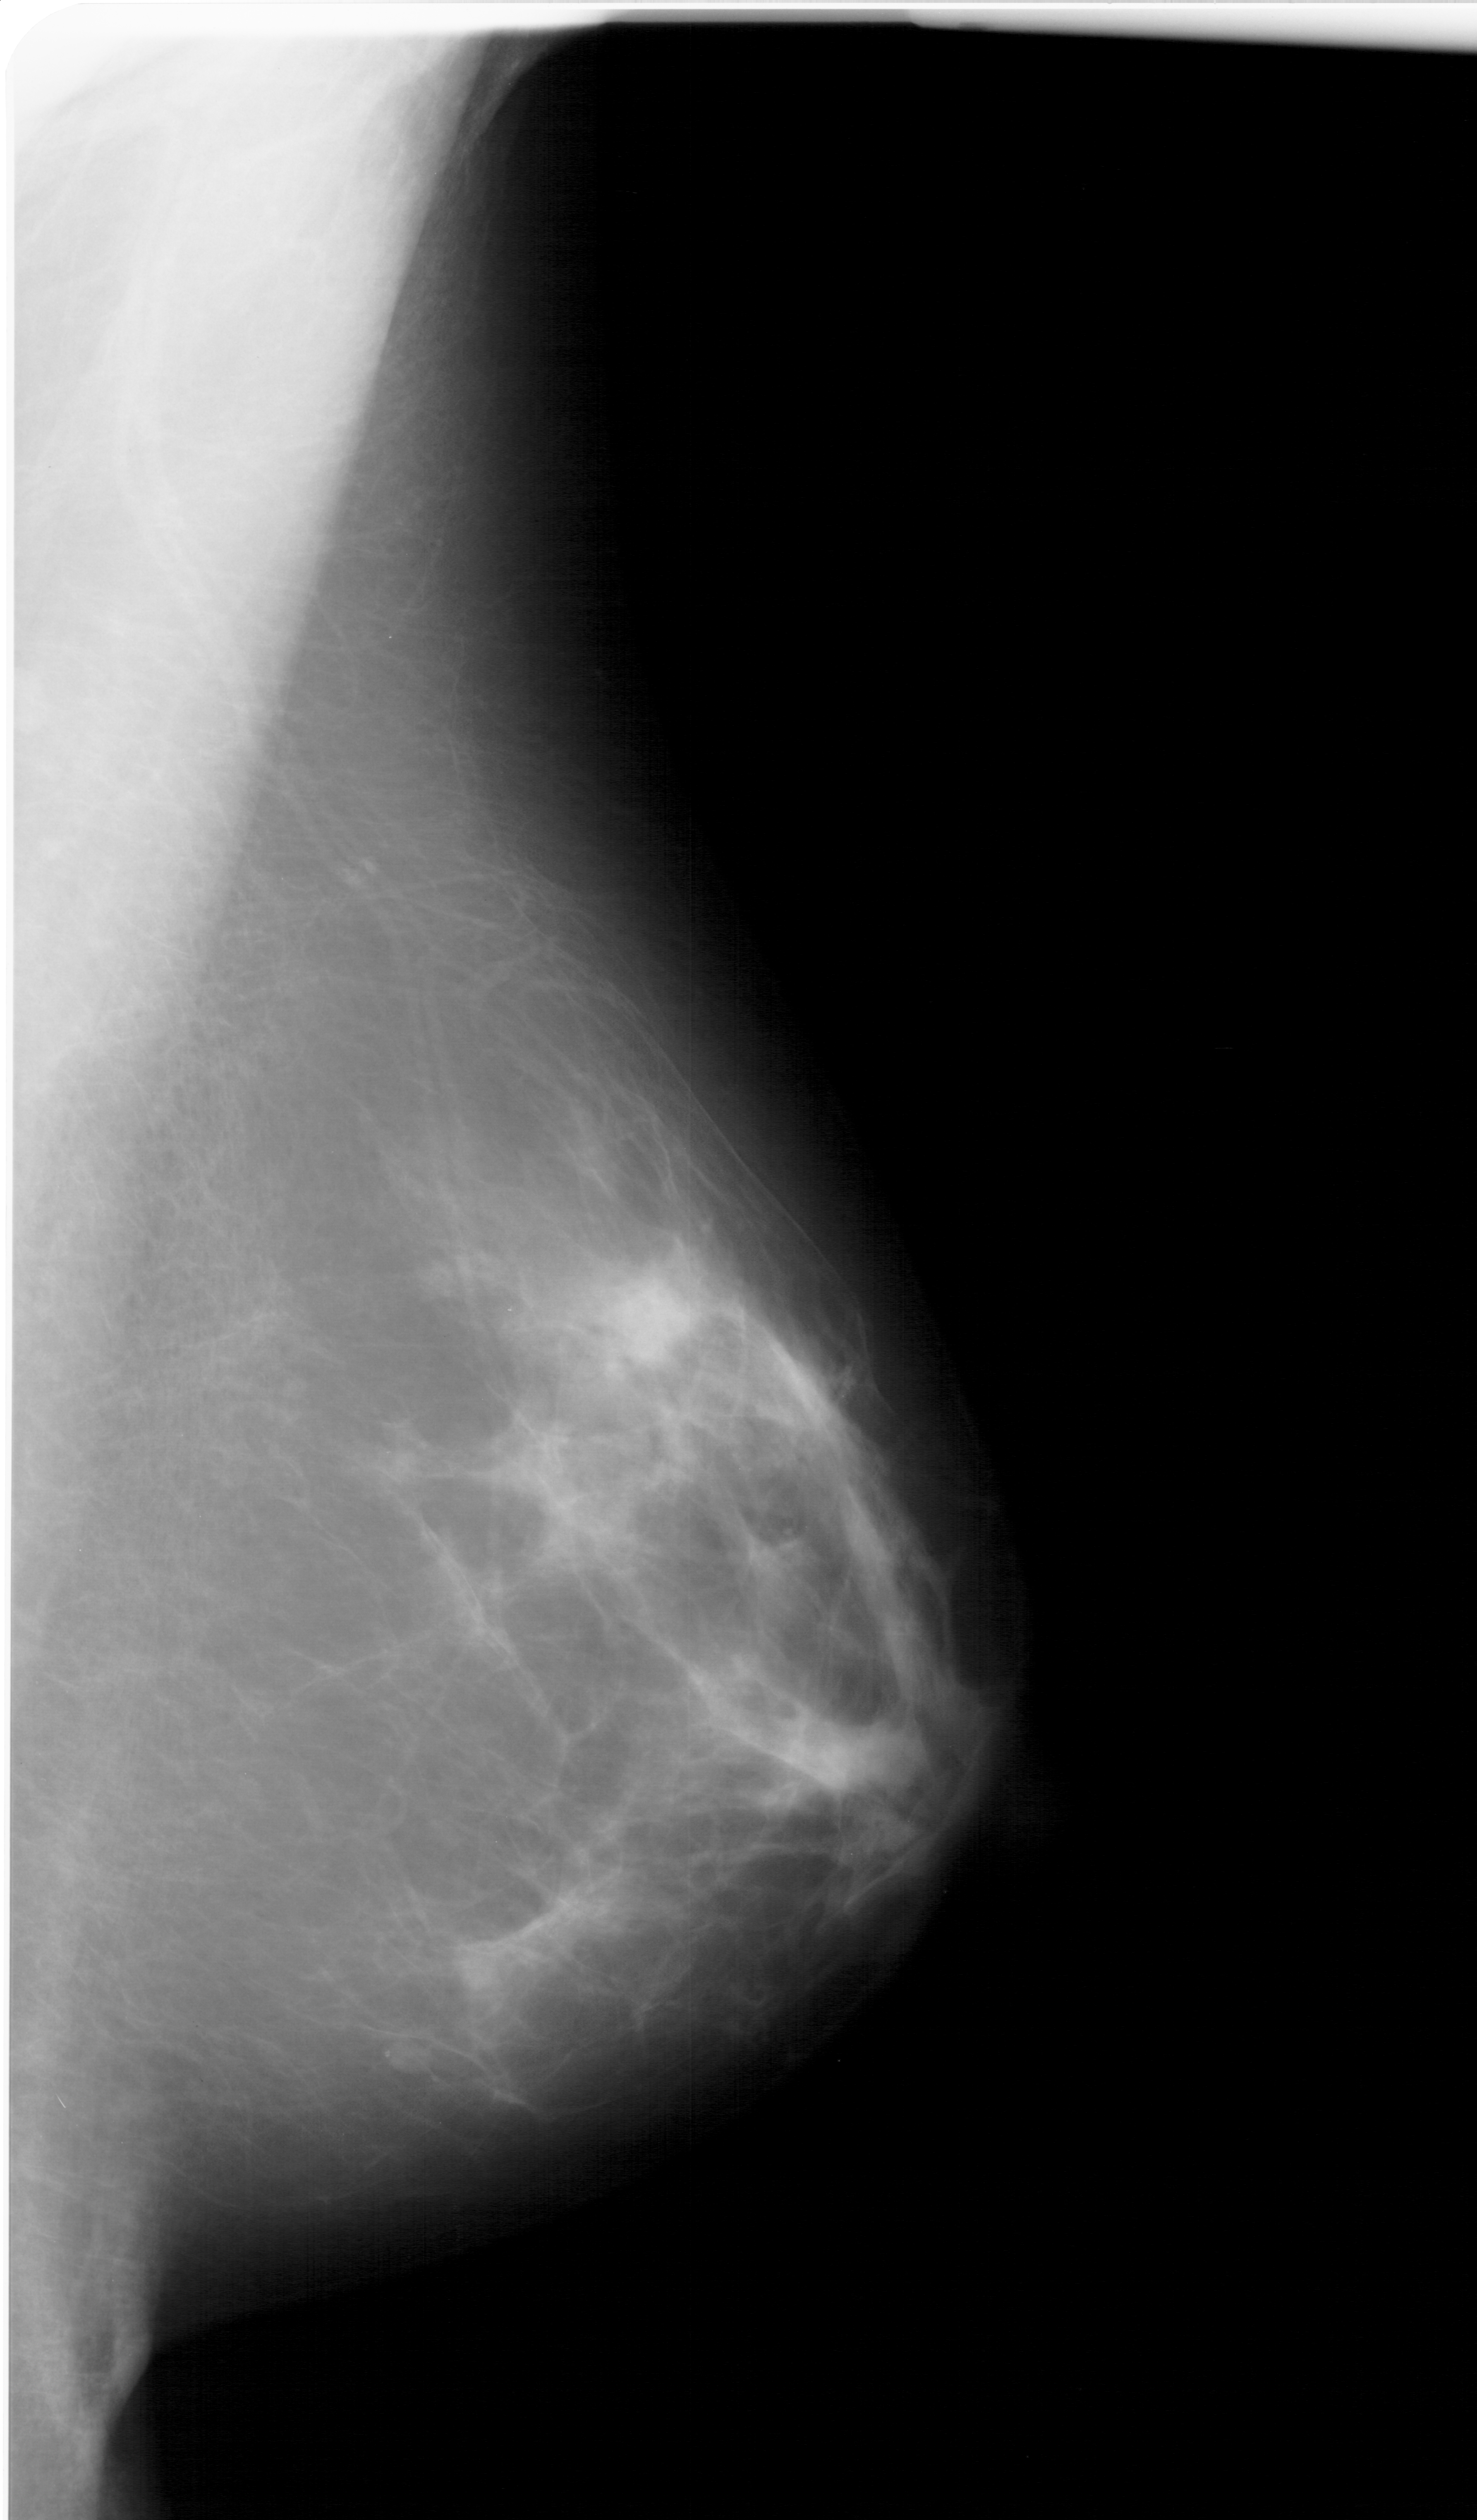
Mammogram (digitized film); right breast; MLO view; BI-RADS breast density category 3 (scale 1–4).
Finding: mass, shape irregular, margins ill defined; BI-RADS assessment category 4; pathology (as recorded): benign.